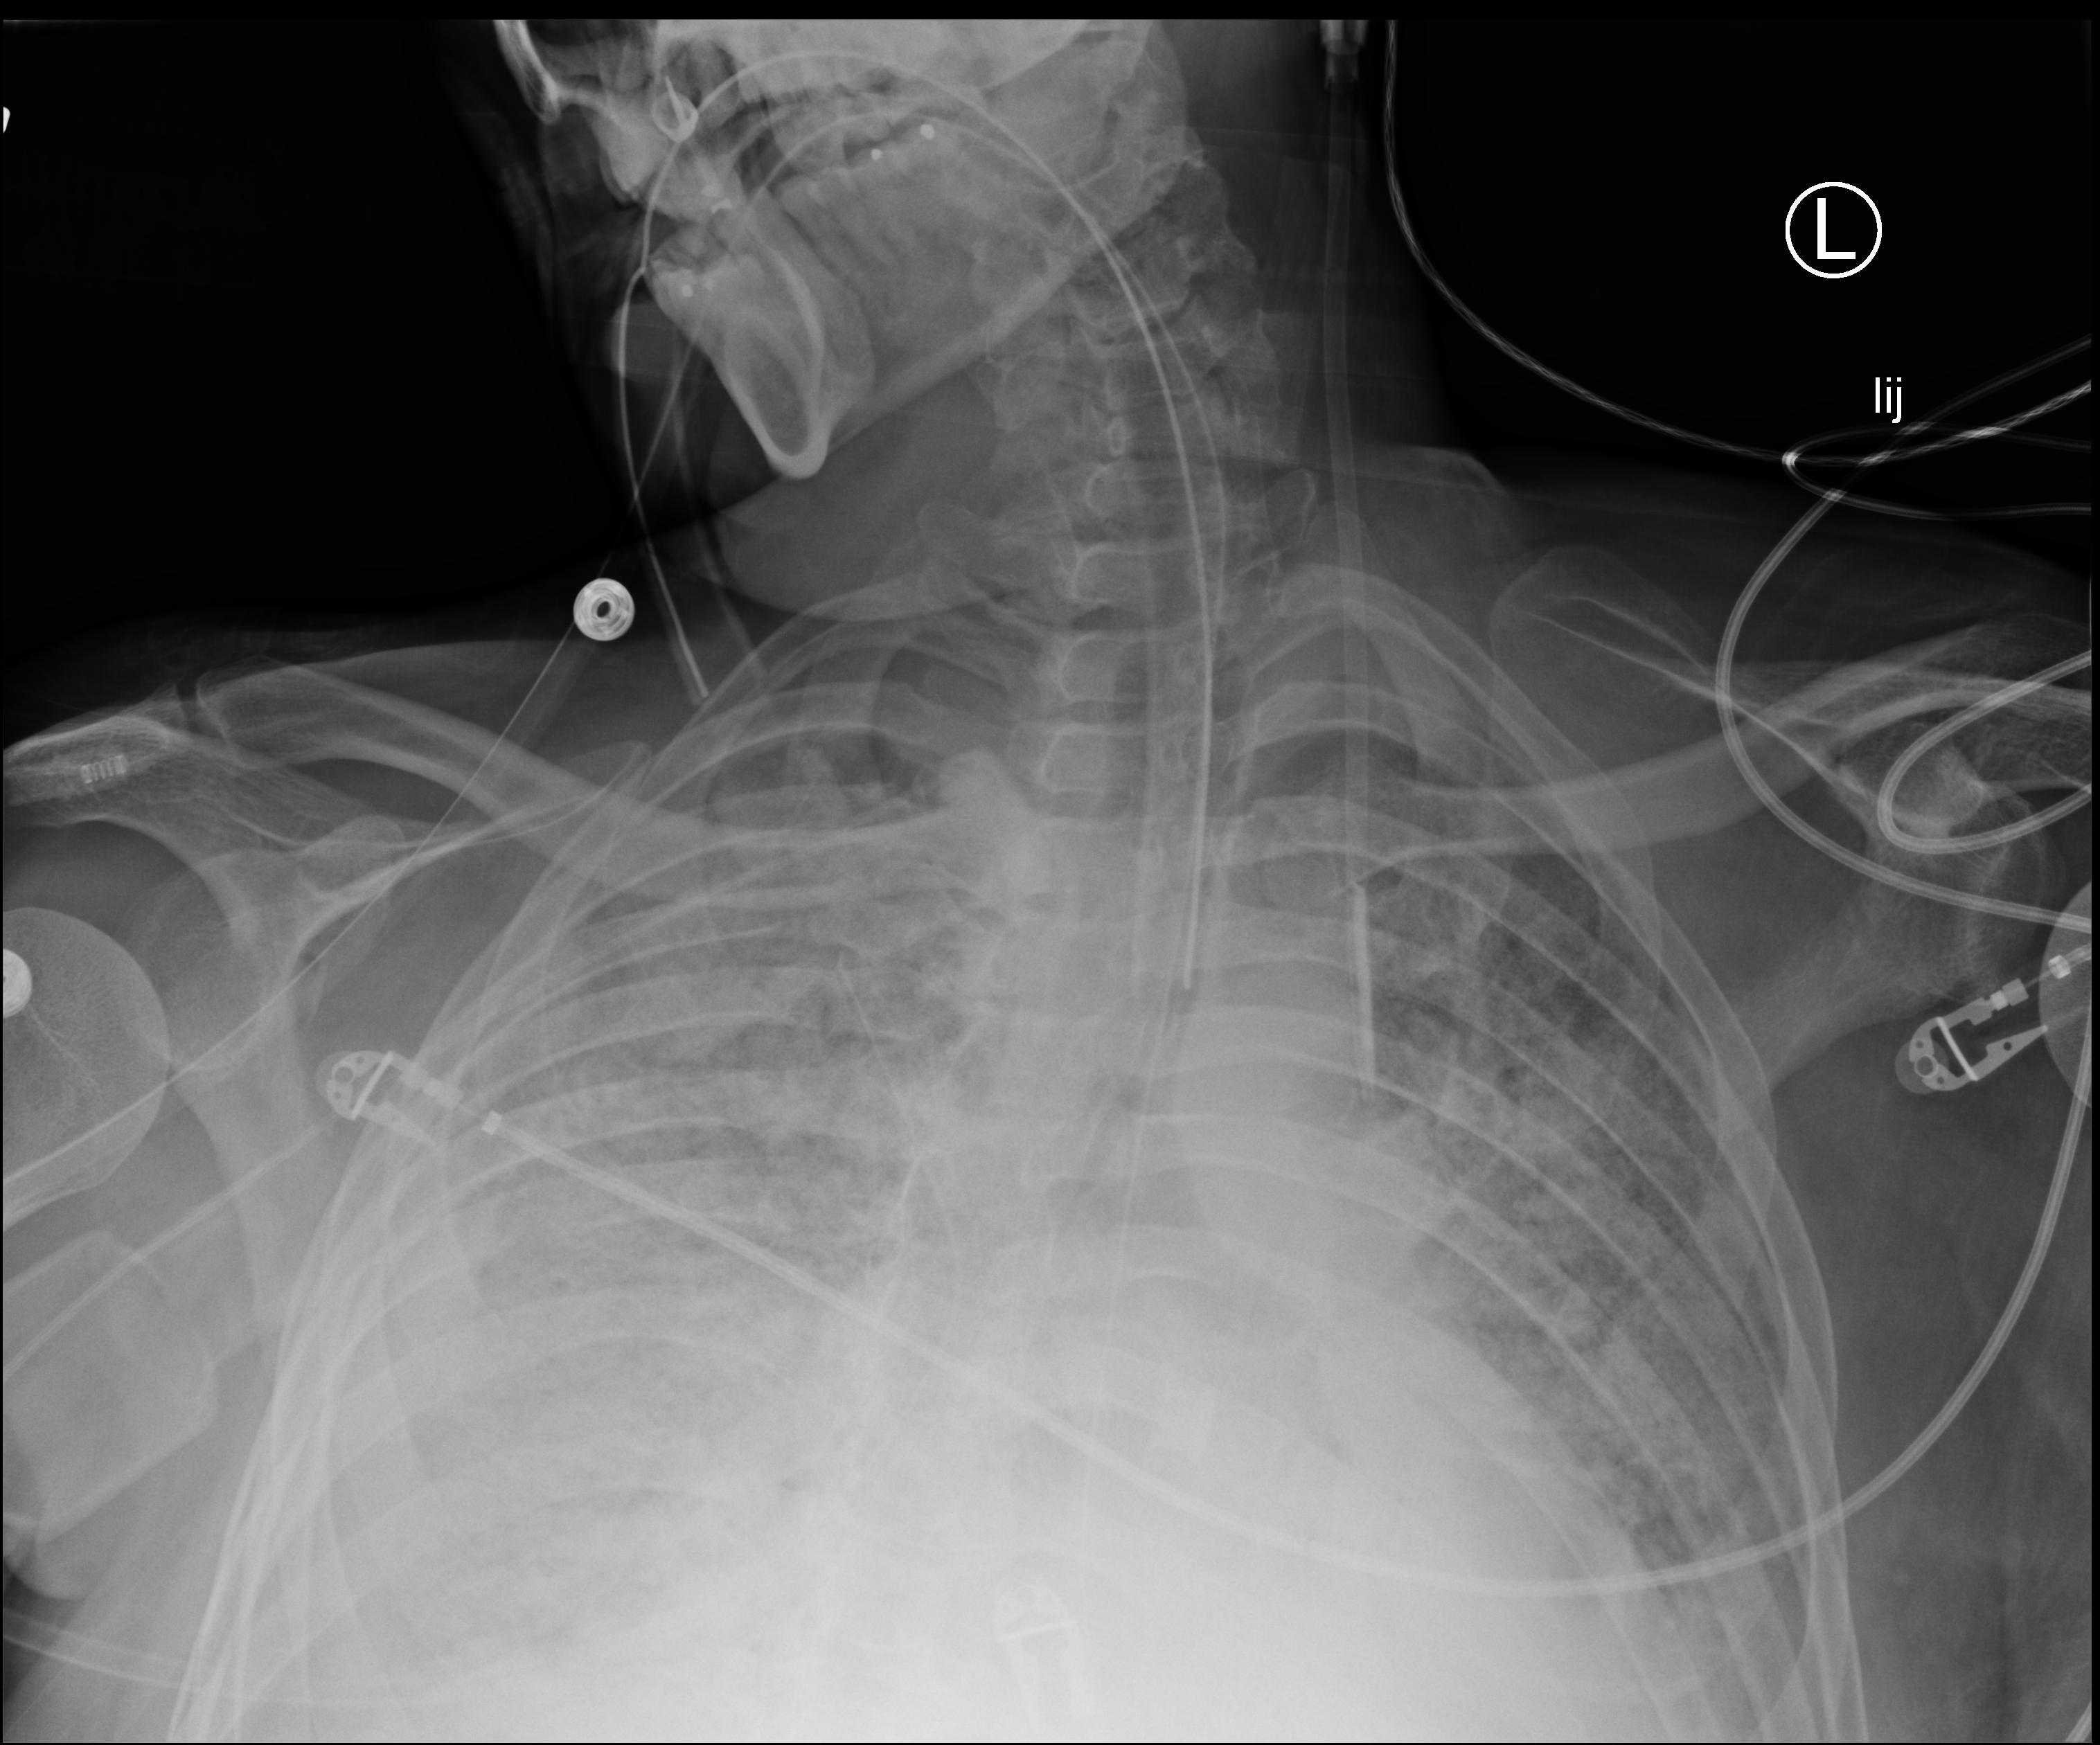
Bedside chest radiograph (computed radiography); anteroposterior (AP) projection. Male patient hospitalised with COVID-19, age 18–59 years.
From the hospital-stay record, not from the radiograph (when in the stay this image was taken is not recorded): admitted to intensive care during this hospital stay: yes.